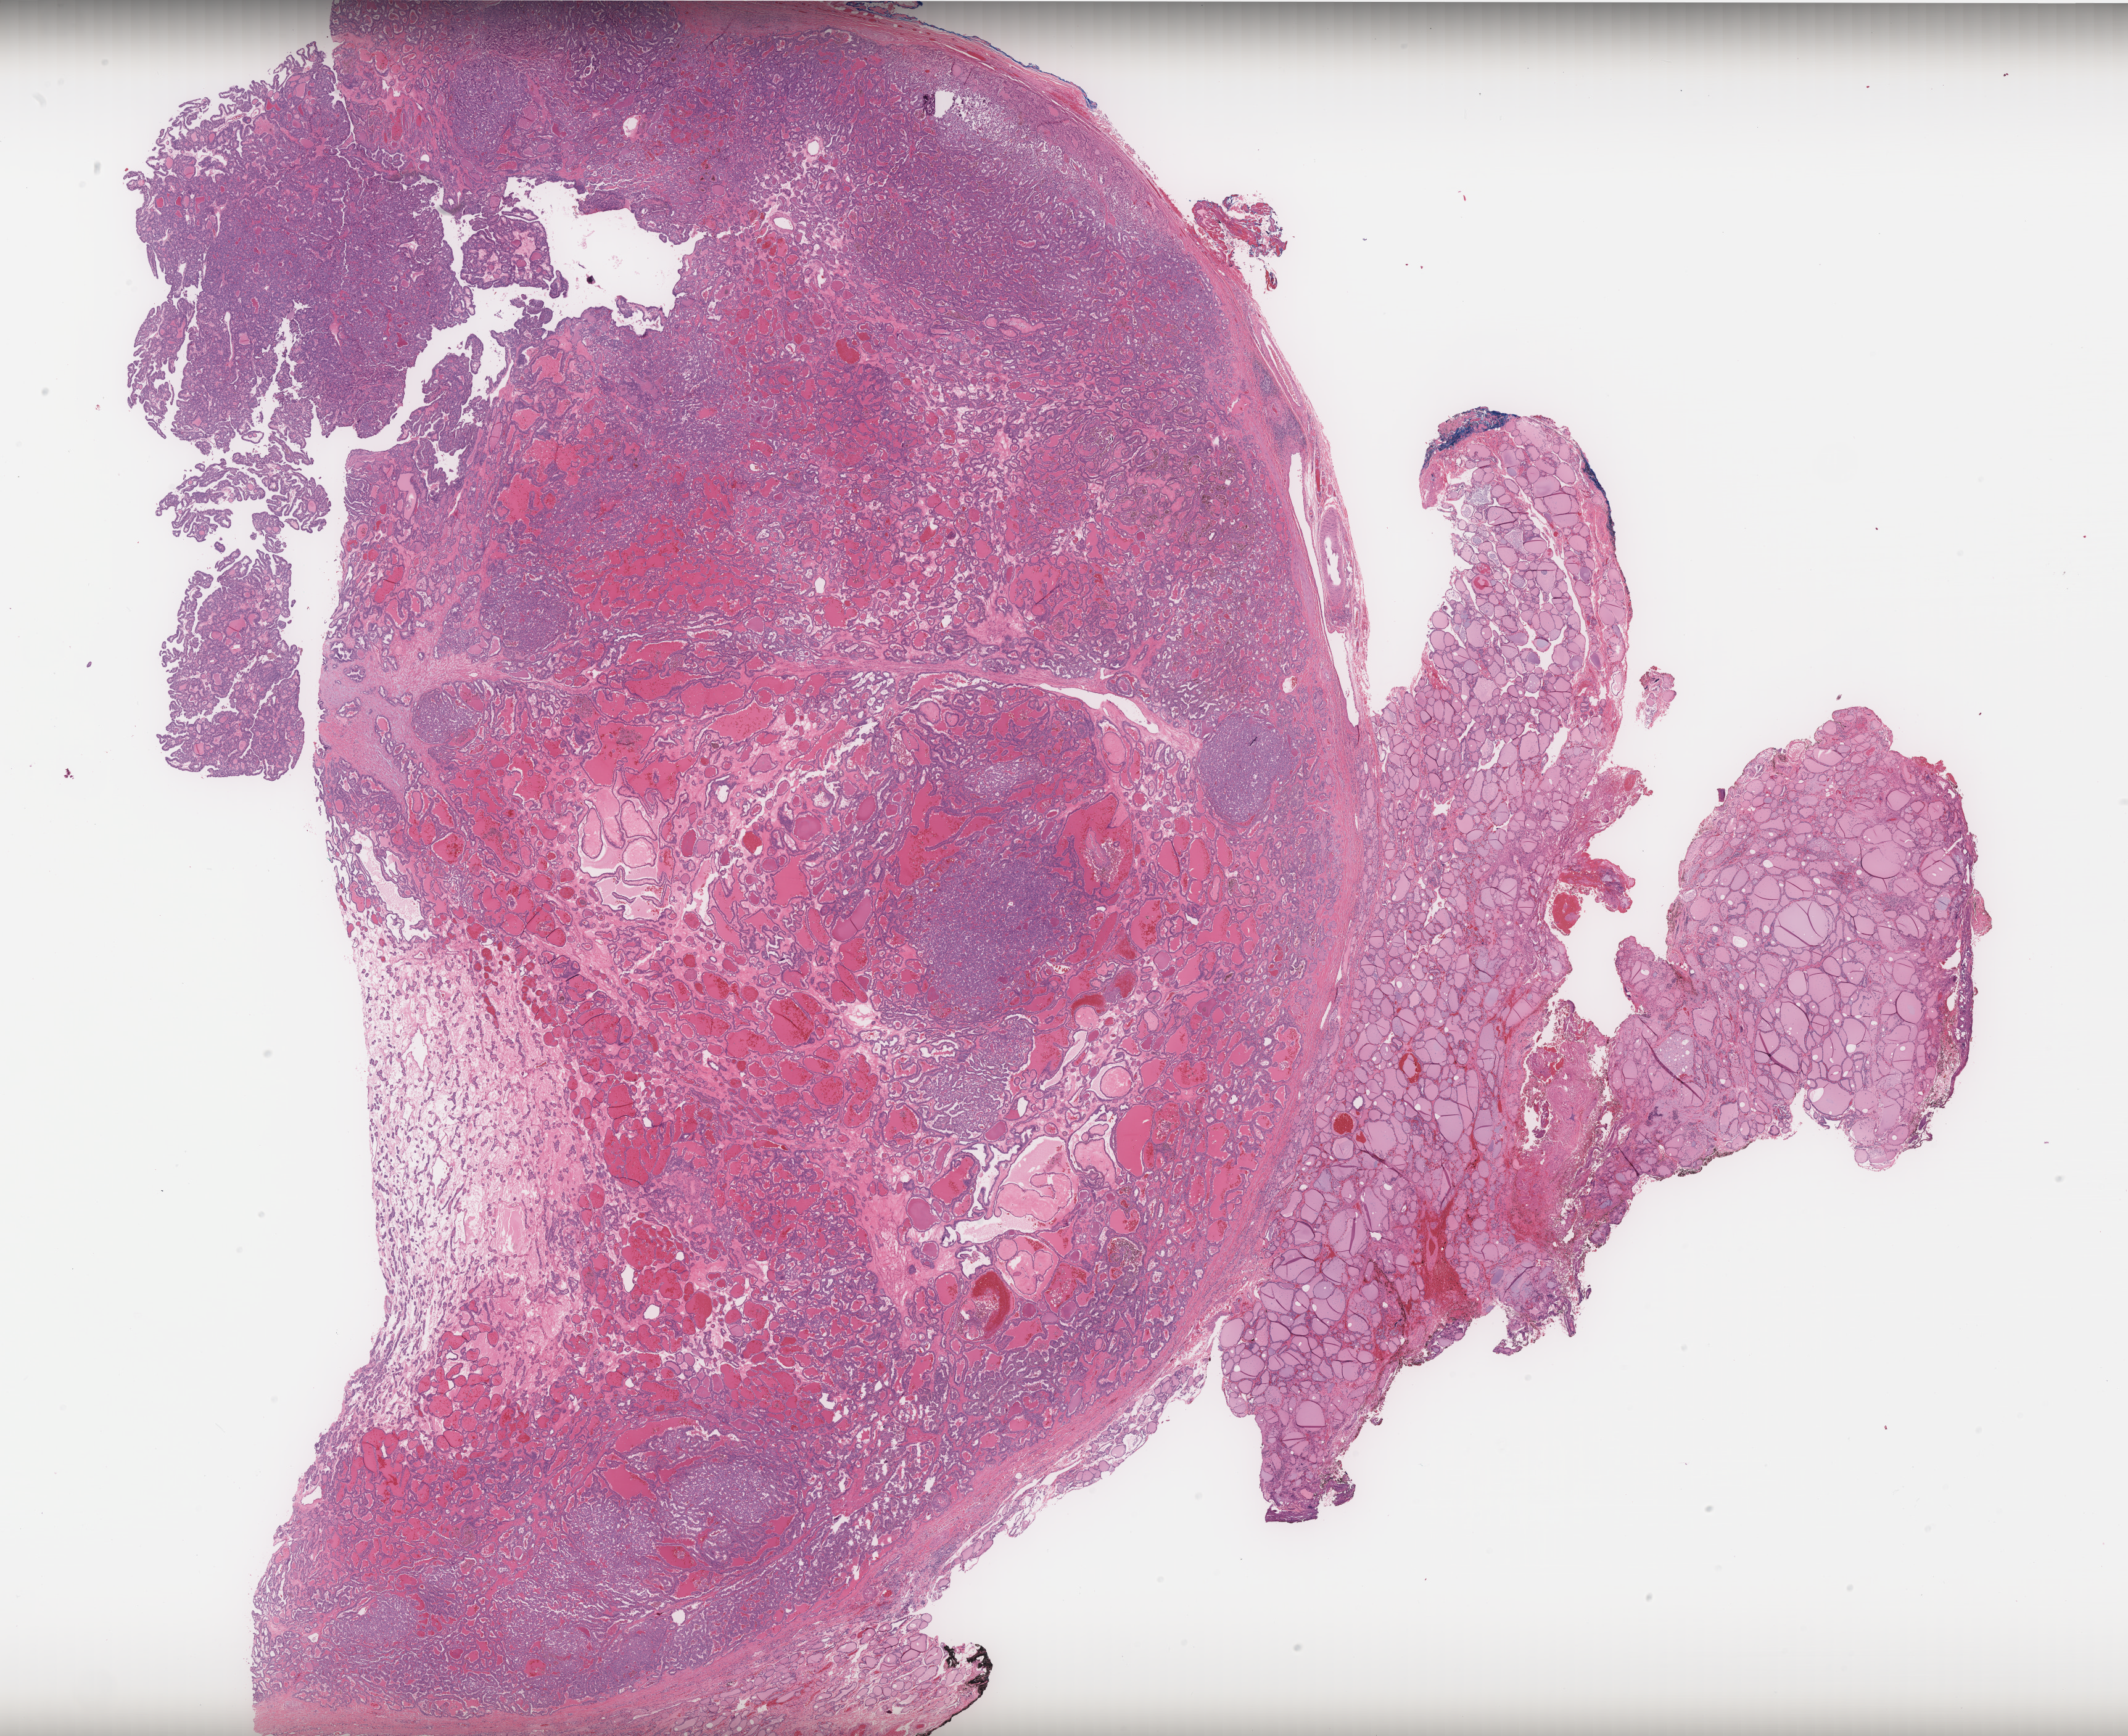
H&E whole-slide image, shown as a low-resolution overview of the whole scanned area (about 27.7 x 22.6 mm, slide scanned at 40x), formalin-fixed paraffin-embedded (FFPE) diagnostic section, thyroid, primary tumour sample. Female, age 61 years at initial diagnosis.
• AJCC pathologic stage: II (6th edition)
• histologic diagnosis: Papillary adenocarcinoma, NOS
• TNM: T2 N0 M0